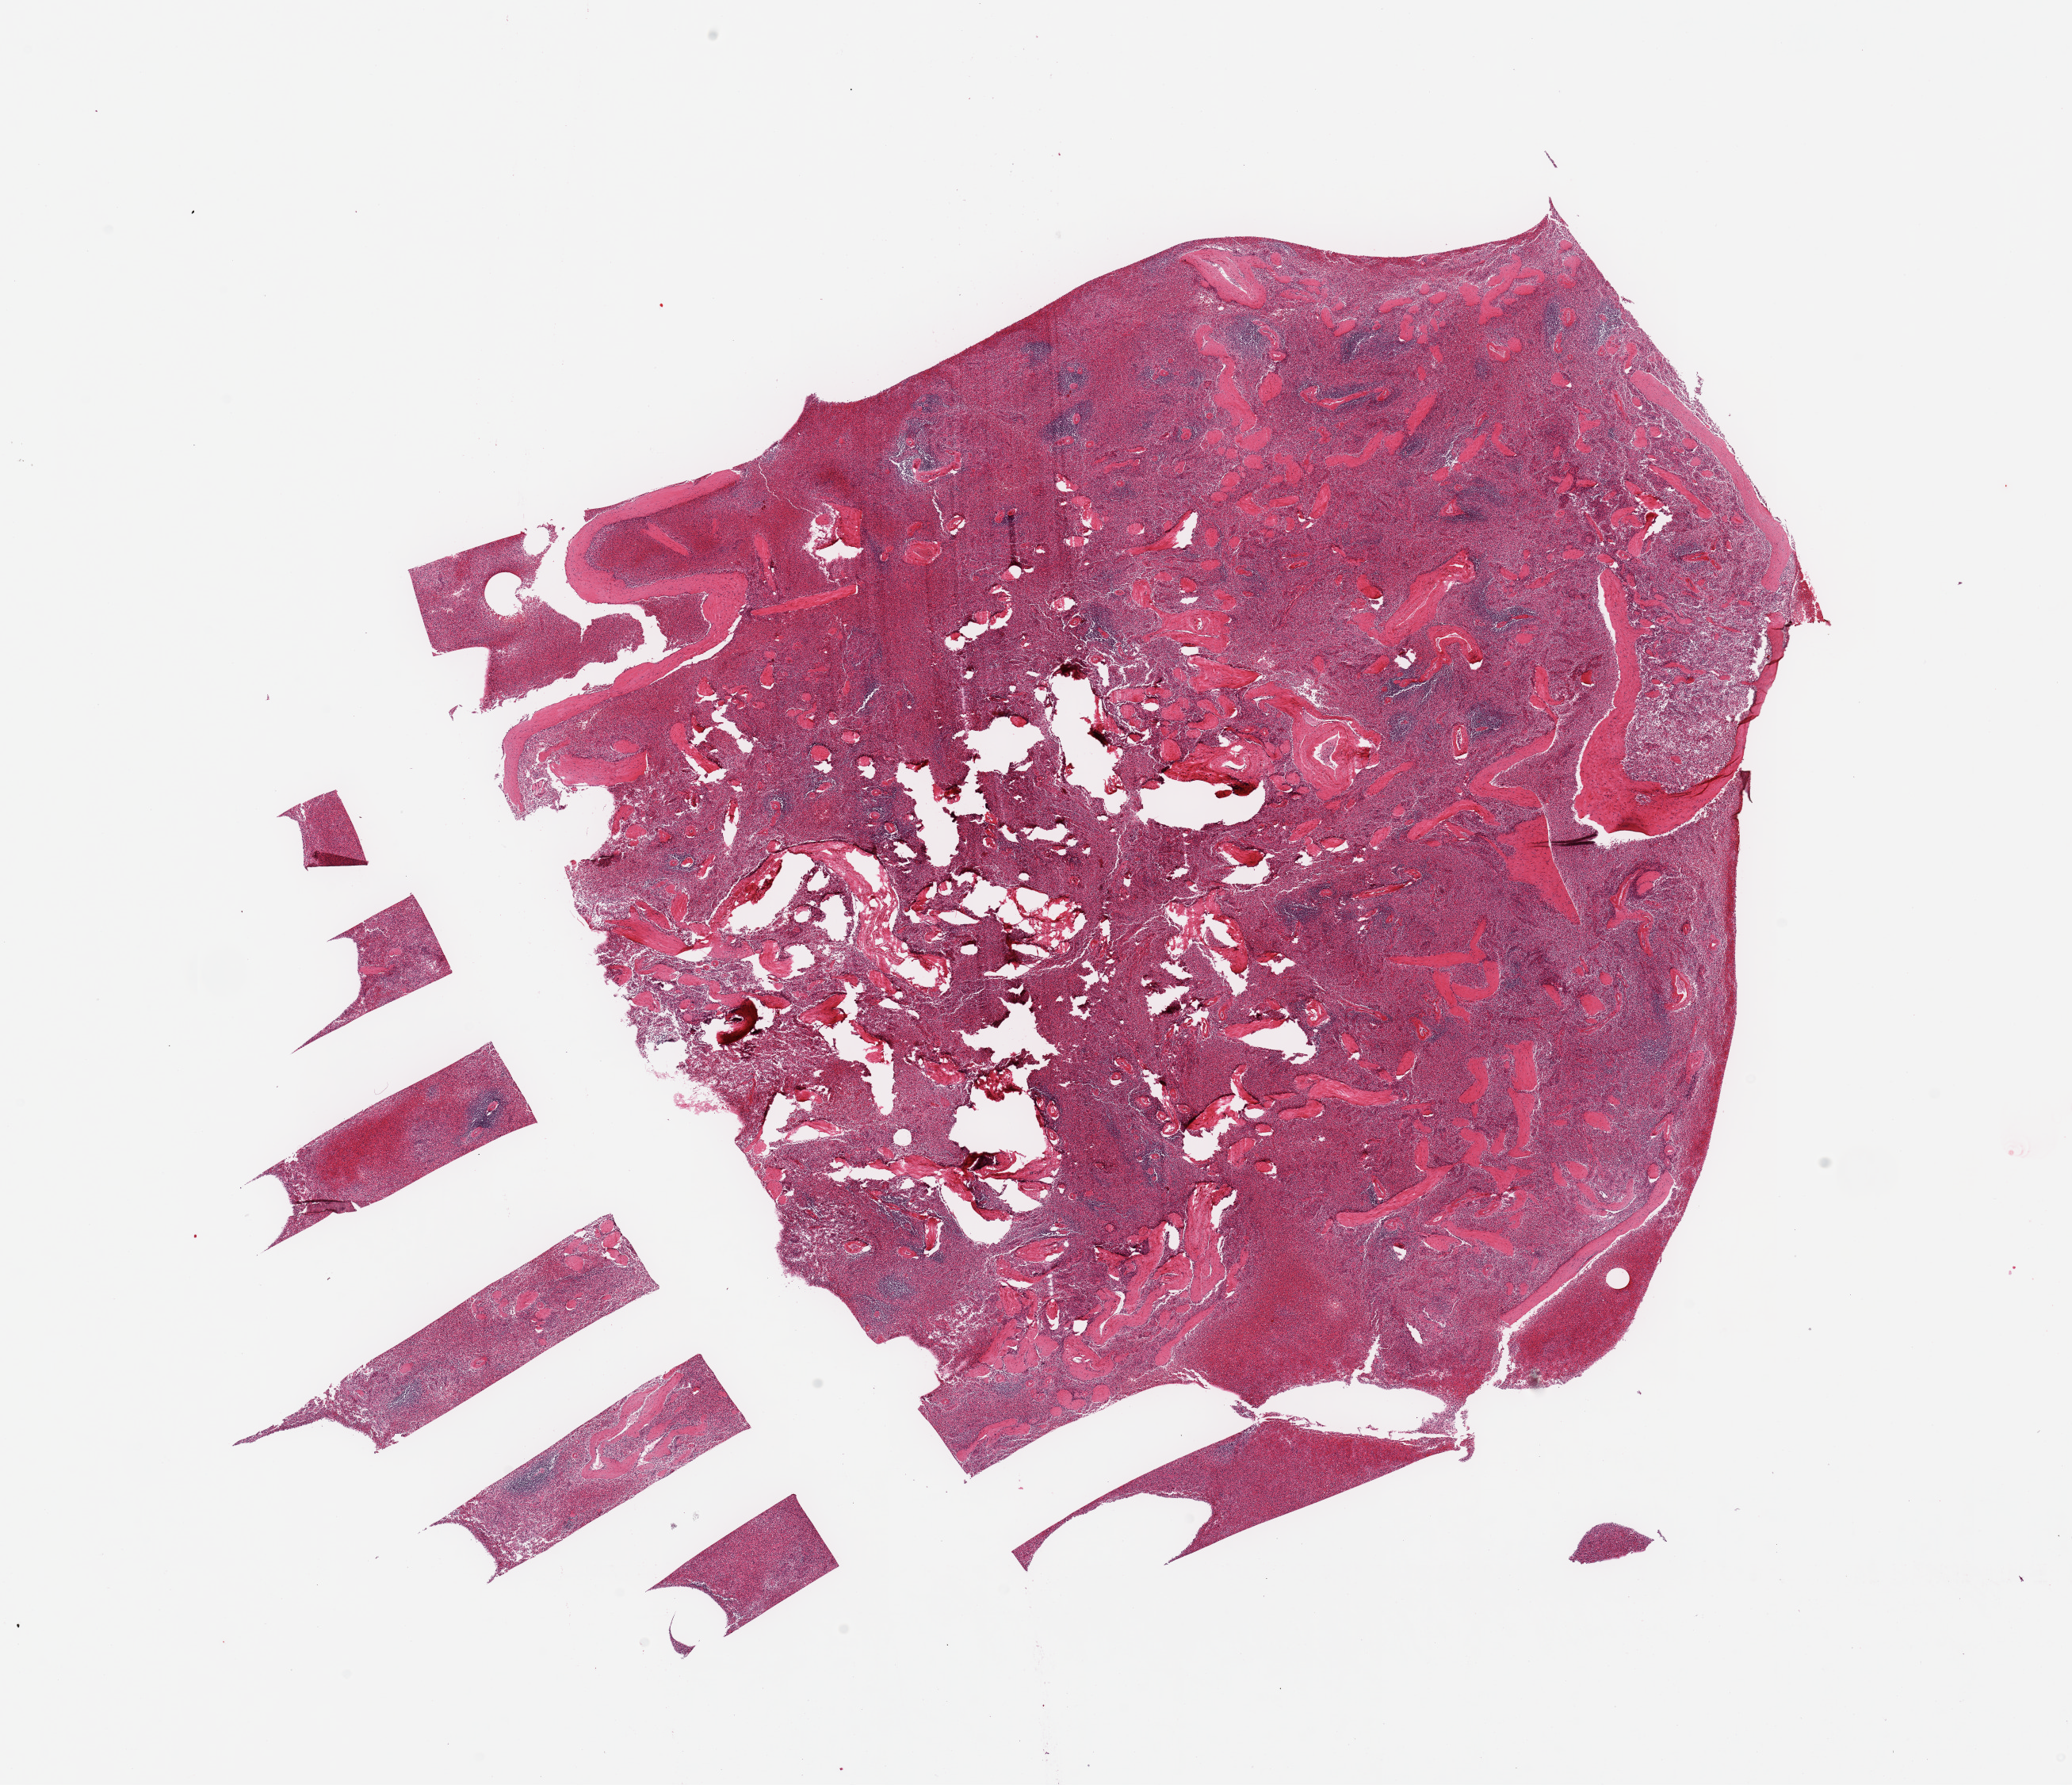
Digitized H&E-stained section — whole scanned area (about 20.7 x 17.8 mm) shown as a low-resolution overview, PAXgene-fixed, paraffin-embedded tissue, target tissue: spleen, donor tissue sample. Donor sex: male.
Reviewer comment on this tissue sample: 1 centrally fragmented piece.